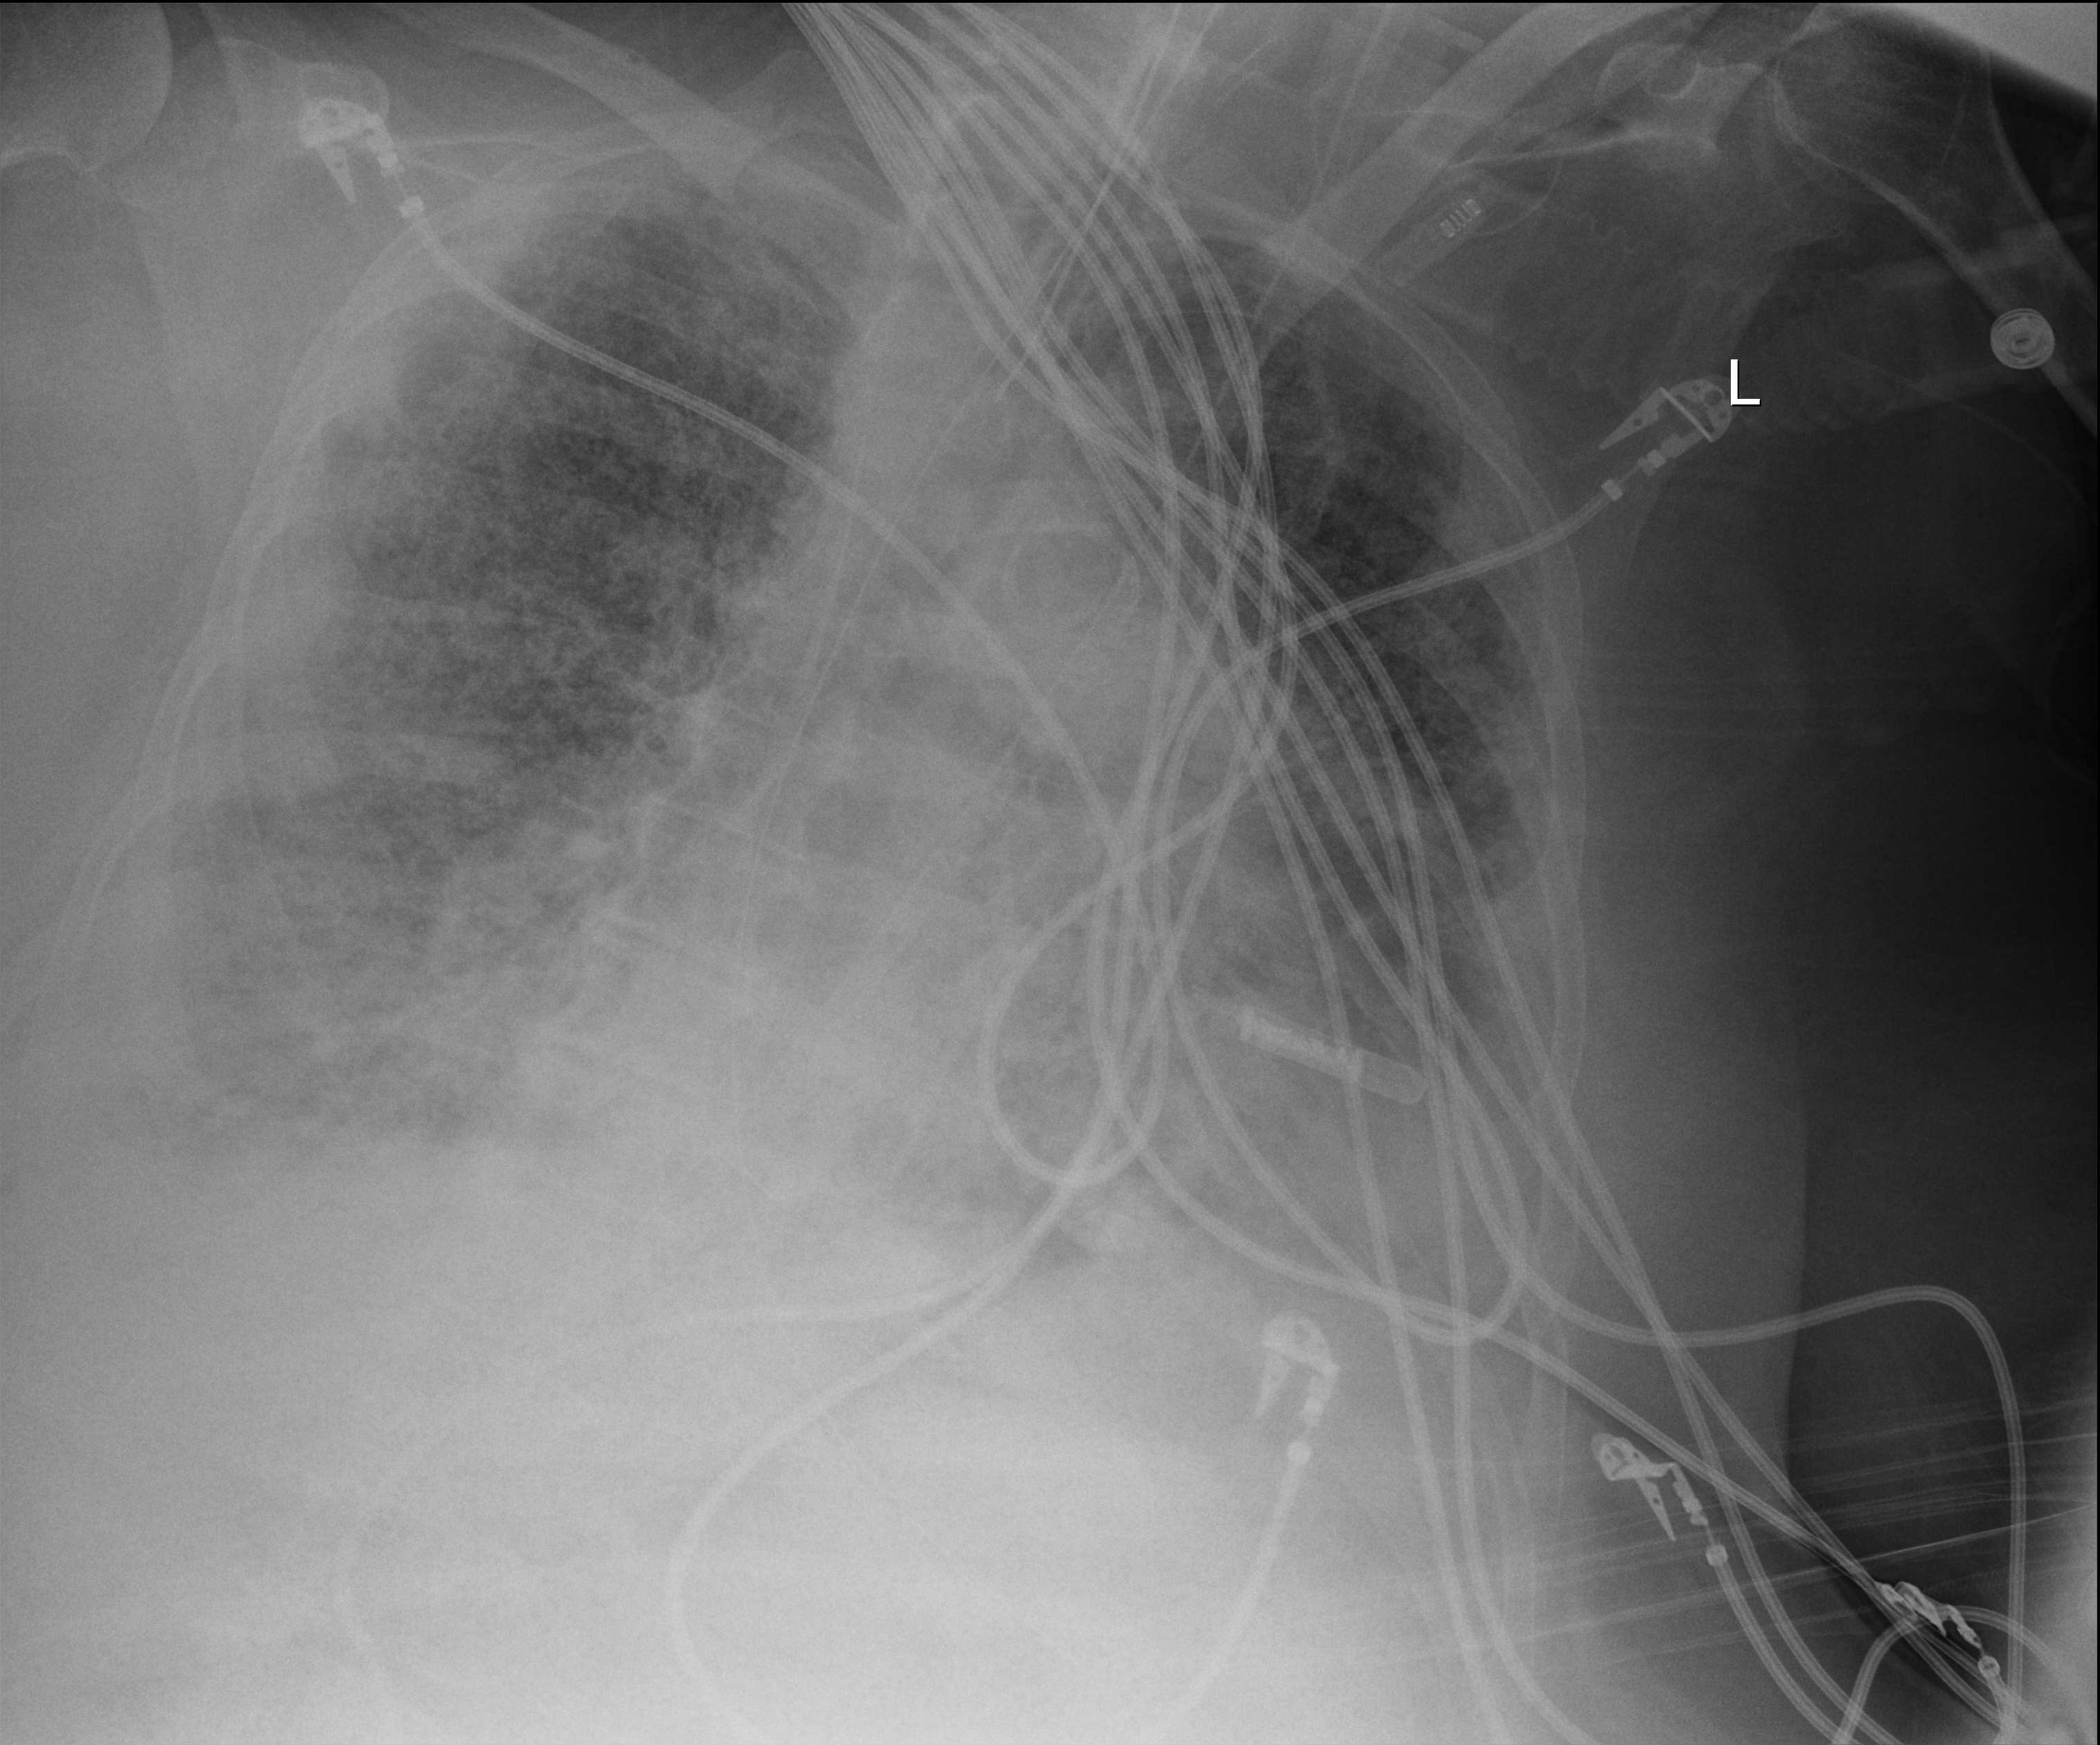
Portable chest radiograph, anteroposterior (AP) projection. Patient hospitalised with COVID-19; female, aged 60–74 years.
From the hospital-stay record, not from the radiograph (when in the stay this image was taken is not recorded): length of hospital stay: 28 days.